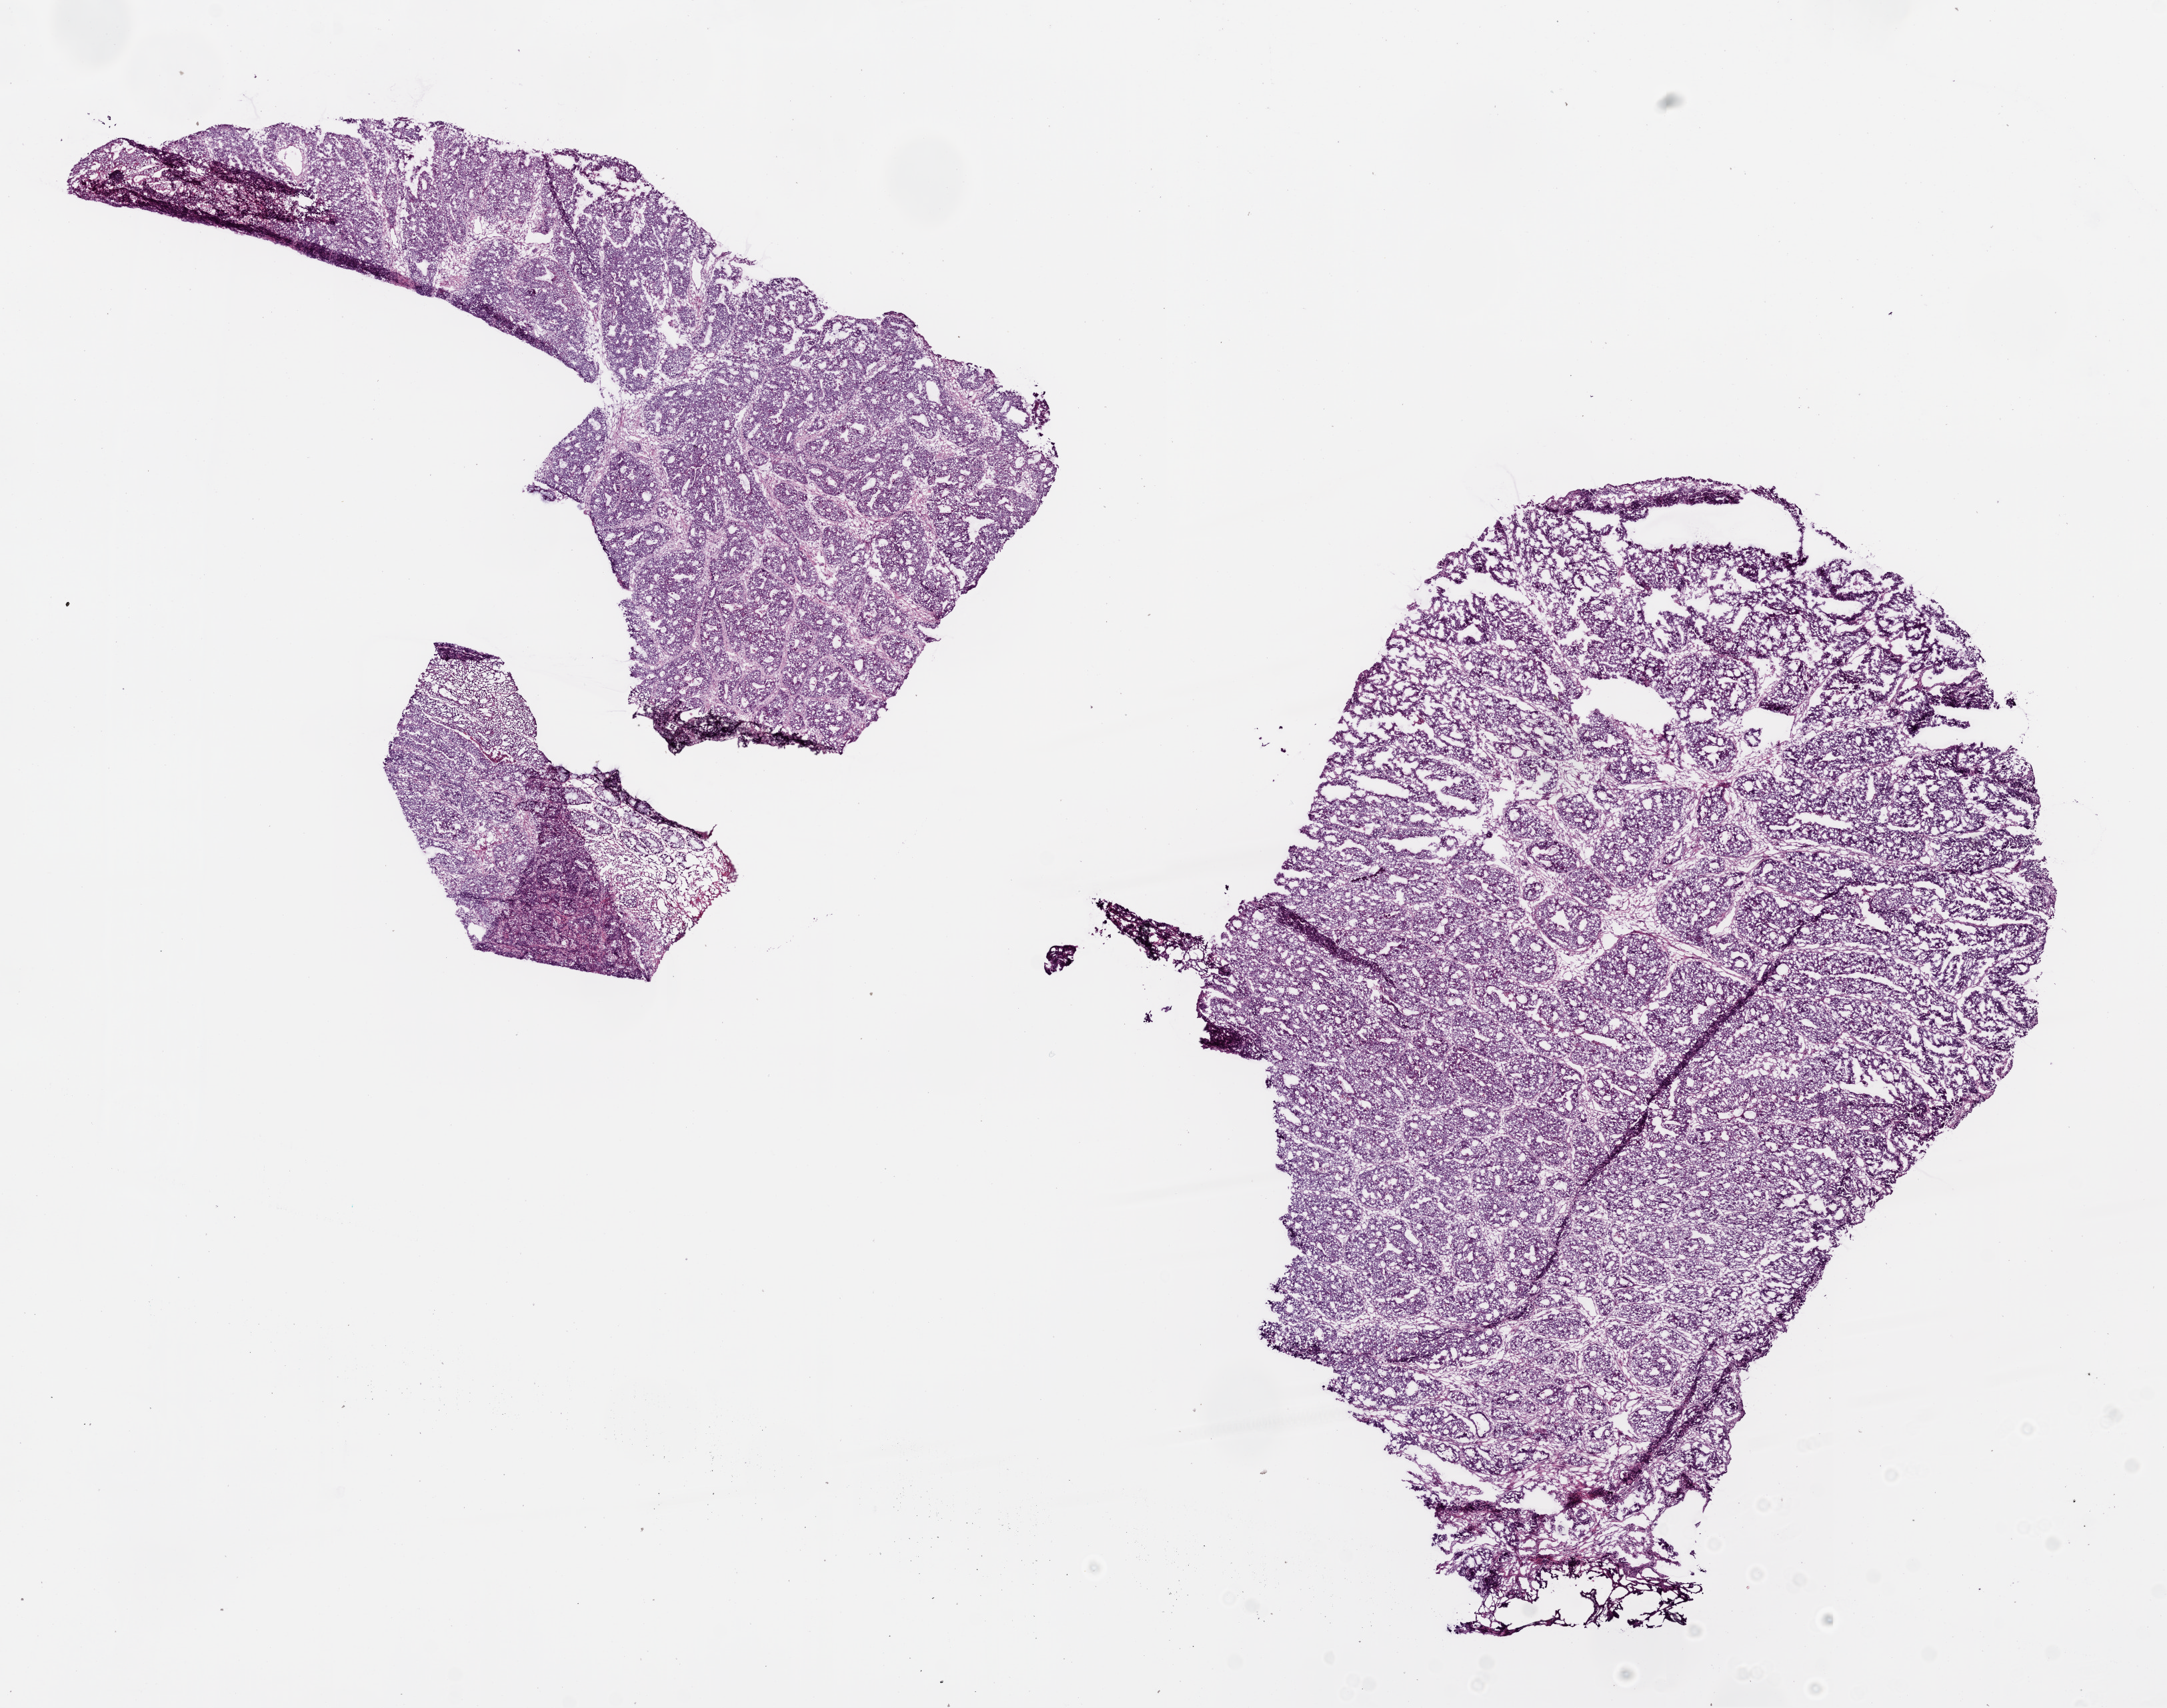
H&E-stained whole-slide image — a low-resolution overview of the entire scanned area, about 13.0 x 10.3 mm (from a 20x scan); frozen section from the bottom of the tissue portion; sample: primary tumour, colon. Female, age 79 years at initial diagnosis. Slide review estimates, as recorded: tumour cells 75%, tumour nuclei 80%, normal cells 10%, stromal cells 10%, necrosis 5%.
Diagnosis: Adenocarcinoma, NOS (ascending colon). AJCC pathologic stage: IIA. TNM: T3 N0 M0.